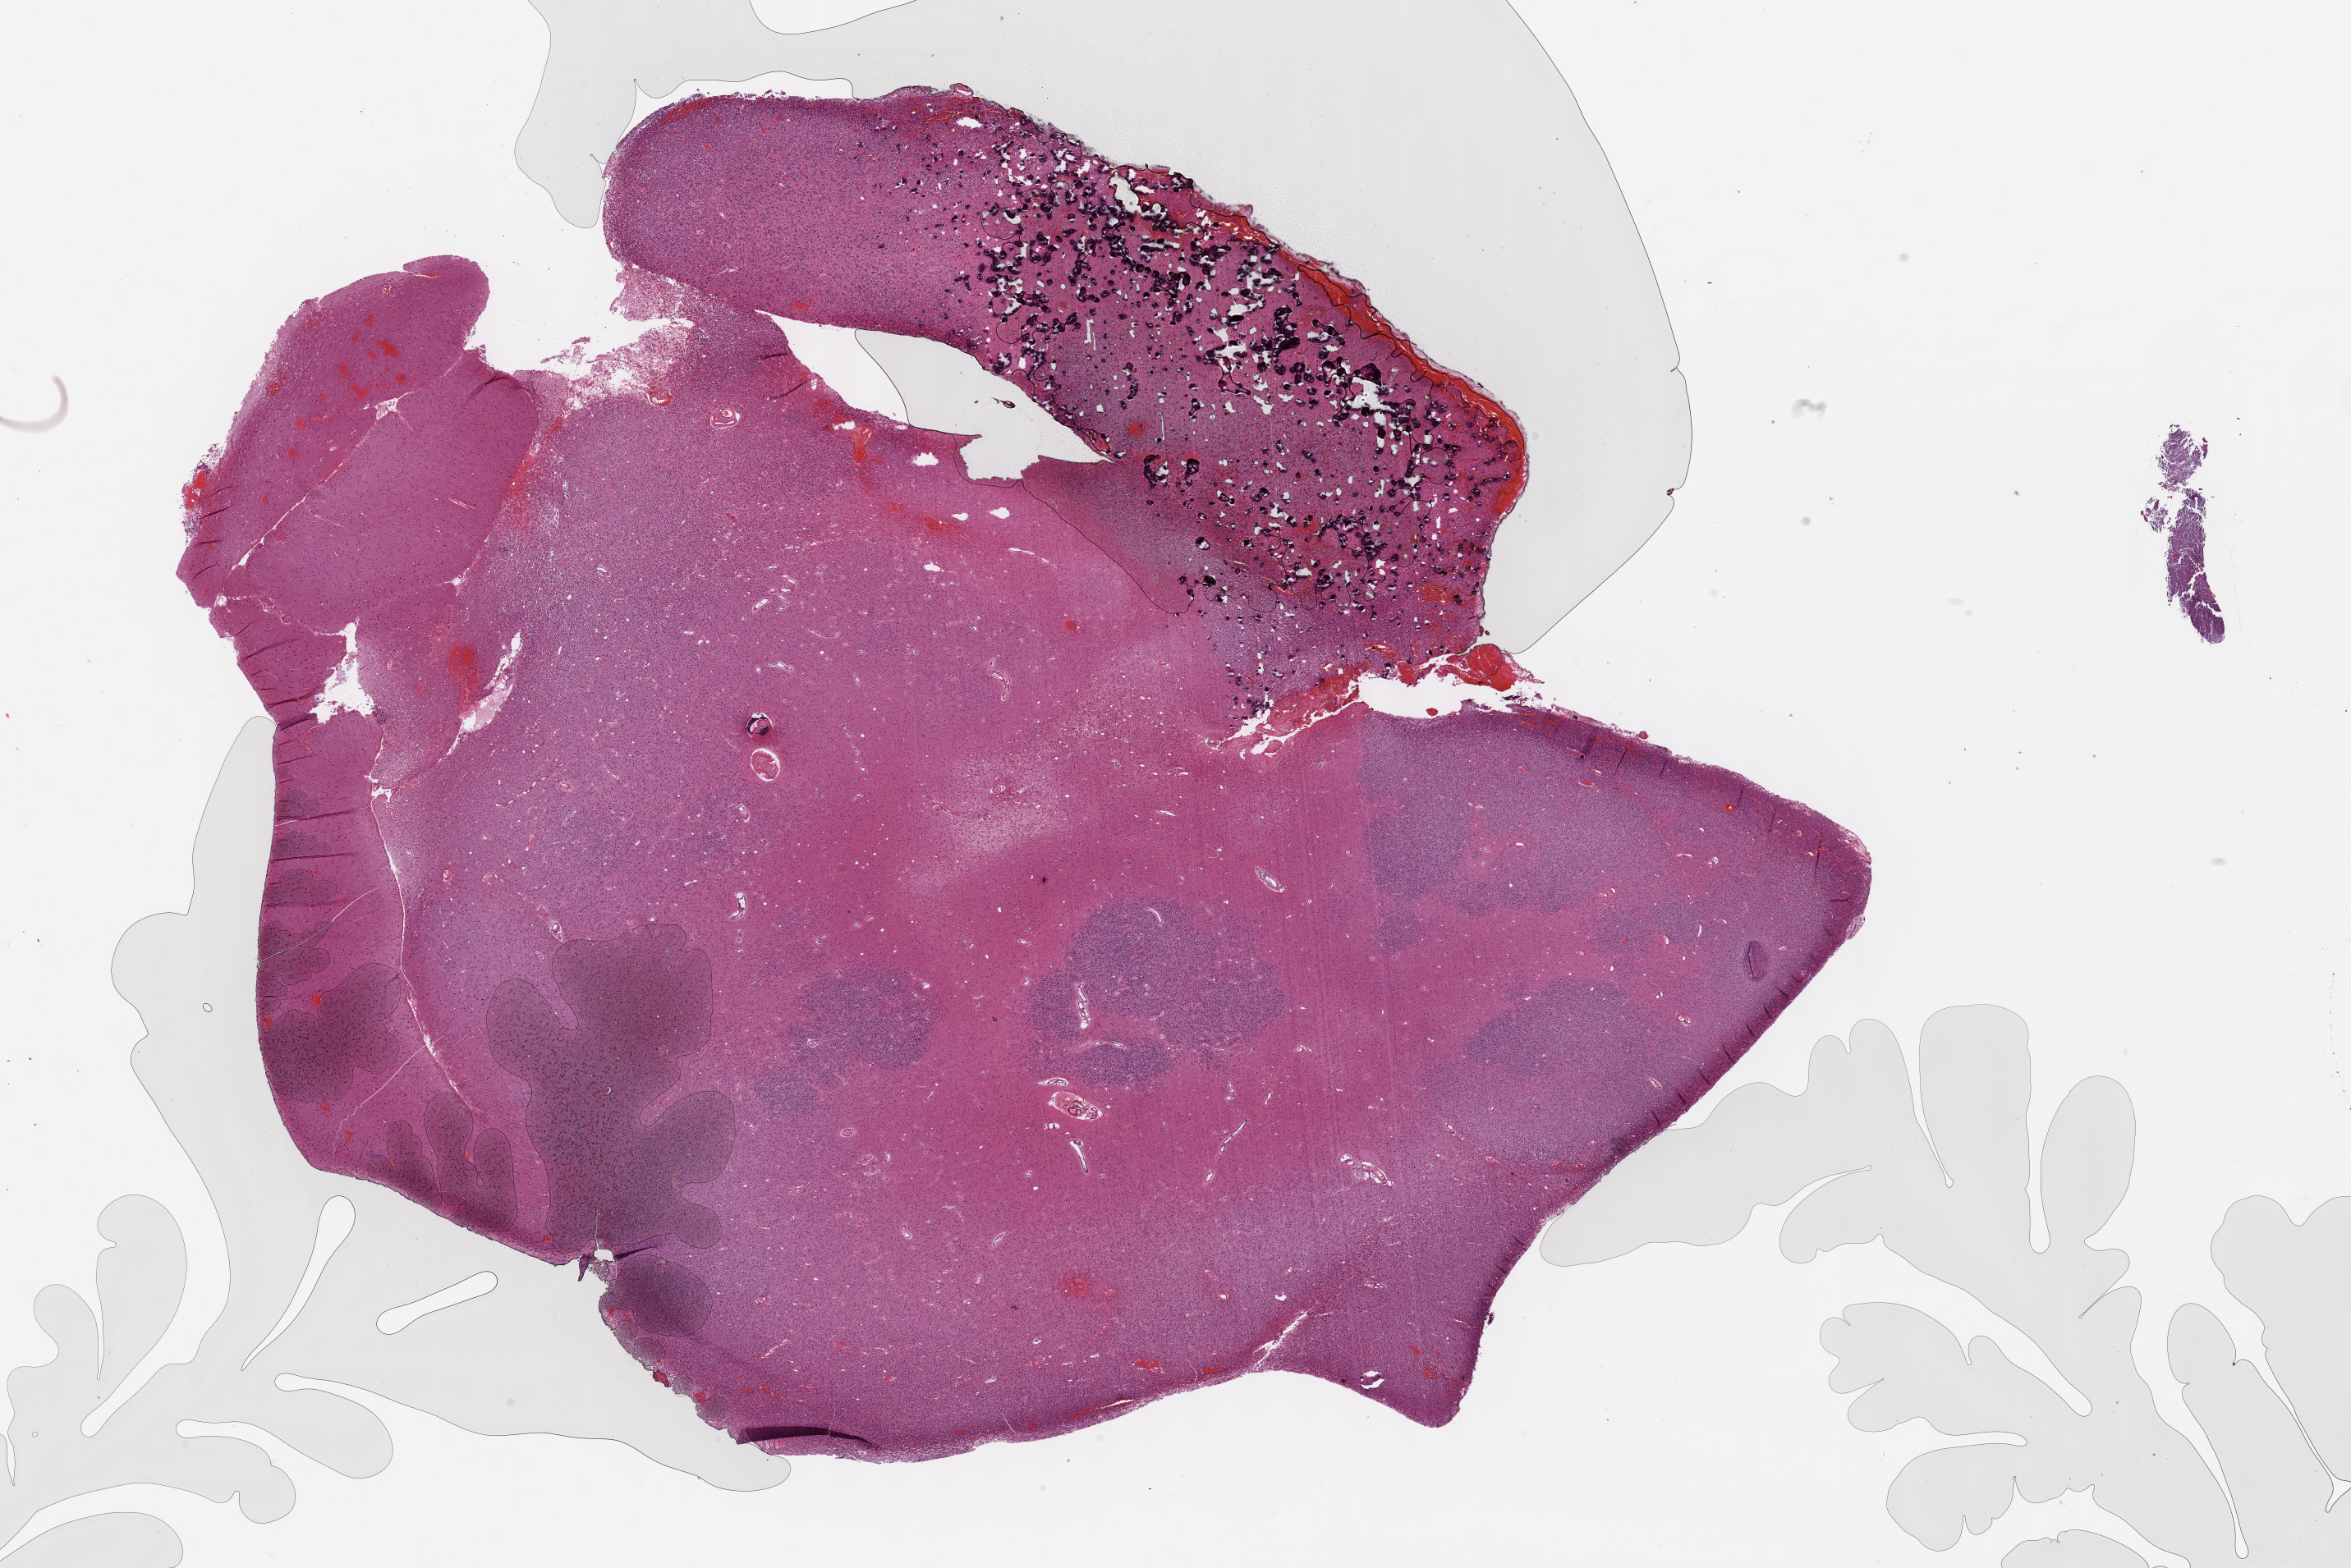
Whole-slide histology image, H&E-stained, low-resolution overview of the scanned area, about 23.2 x 15.4 mm. Formalin-fixed paraffin-embedded (FFPE) diagnostic section. Primary tumour sample from the brain. Male patient; age at initial diagnosis 53 years. Histologic grade: G3 (poorly differentiated).
Histologic diagnosis: Oligodendroglioma, anaplastic (cerebrum).